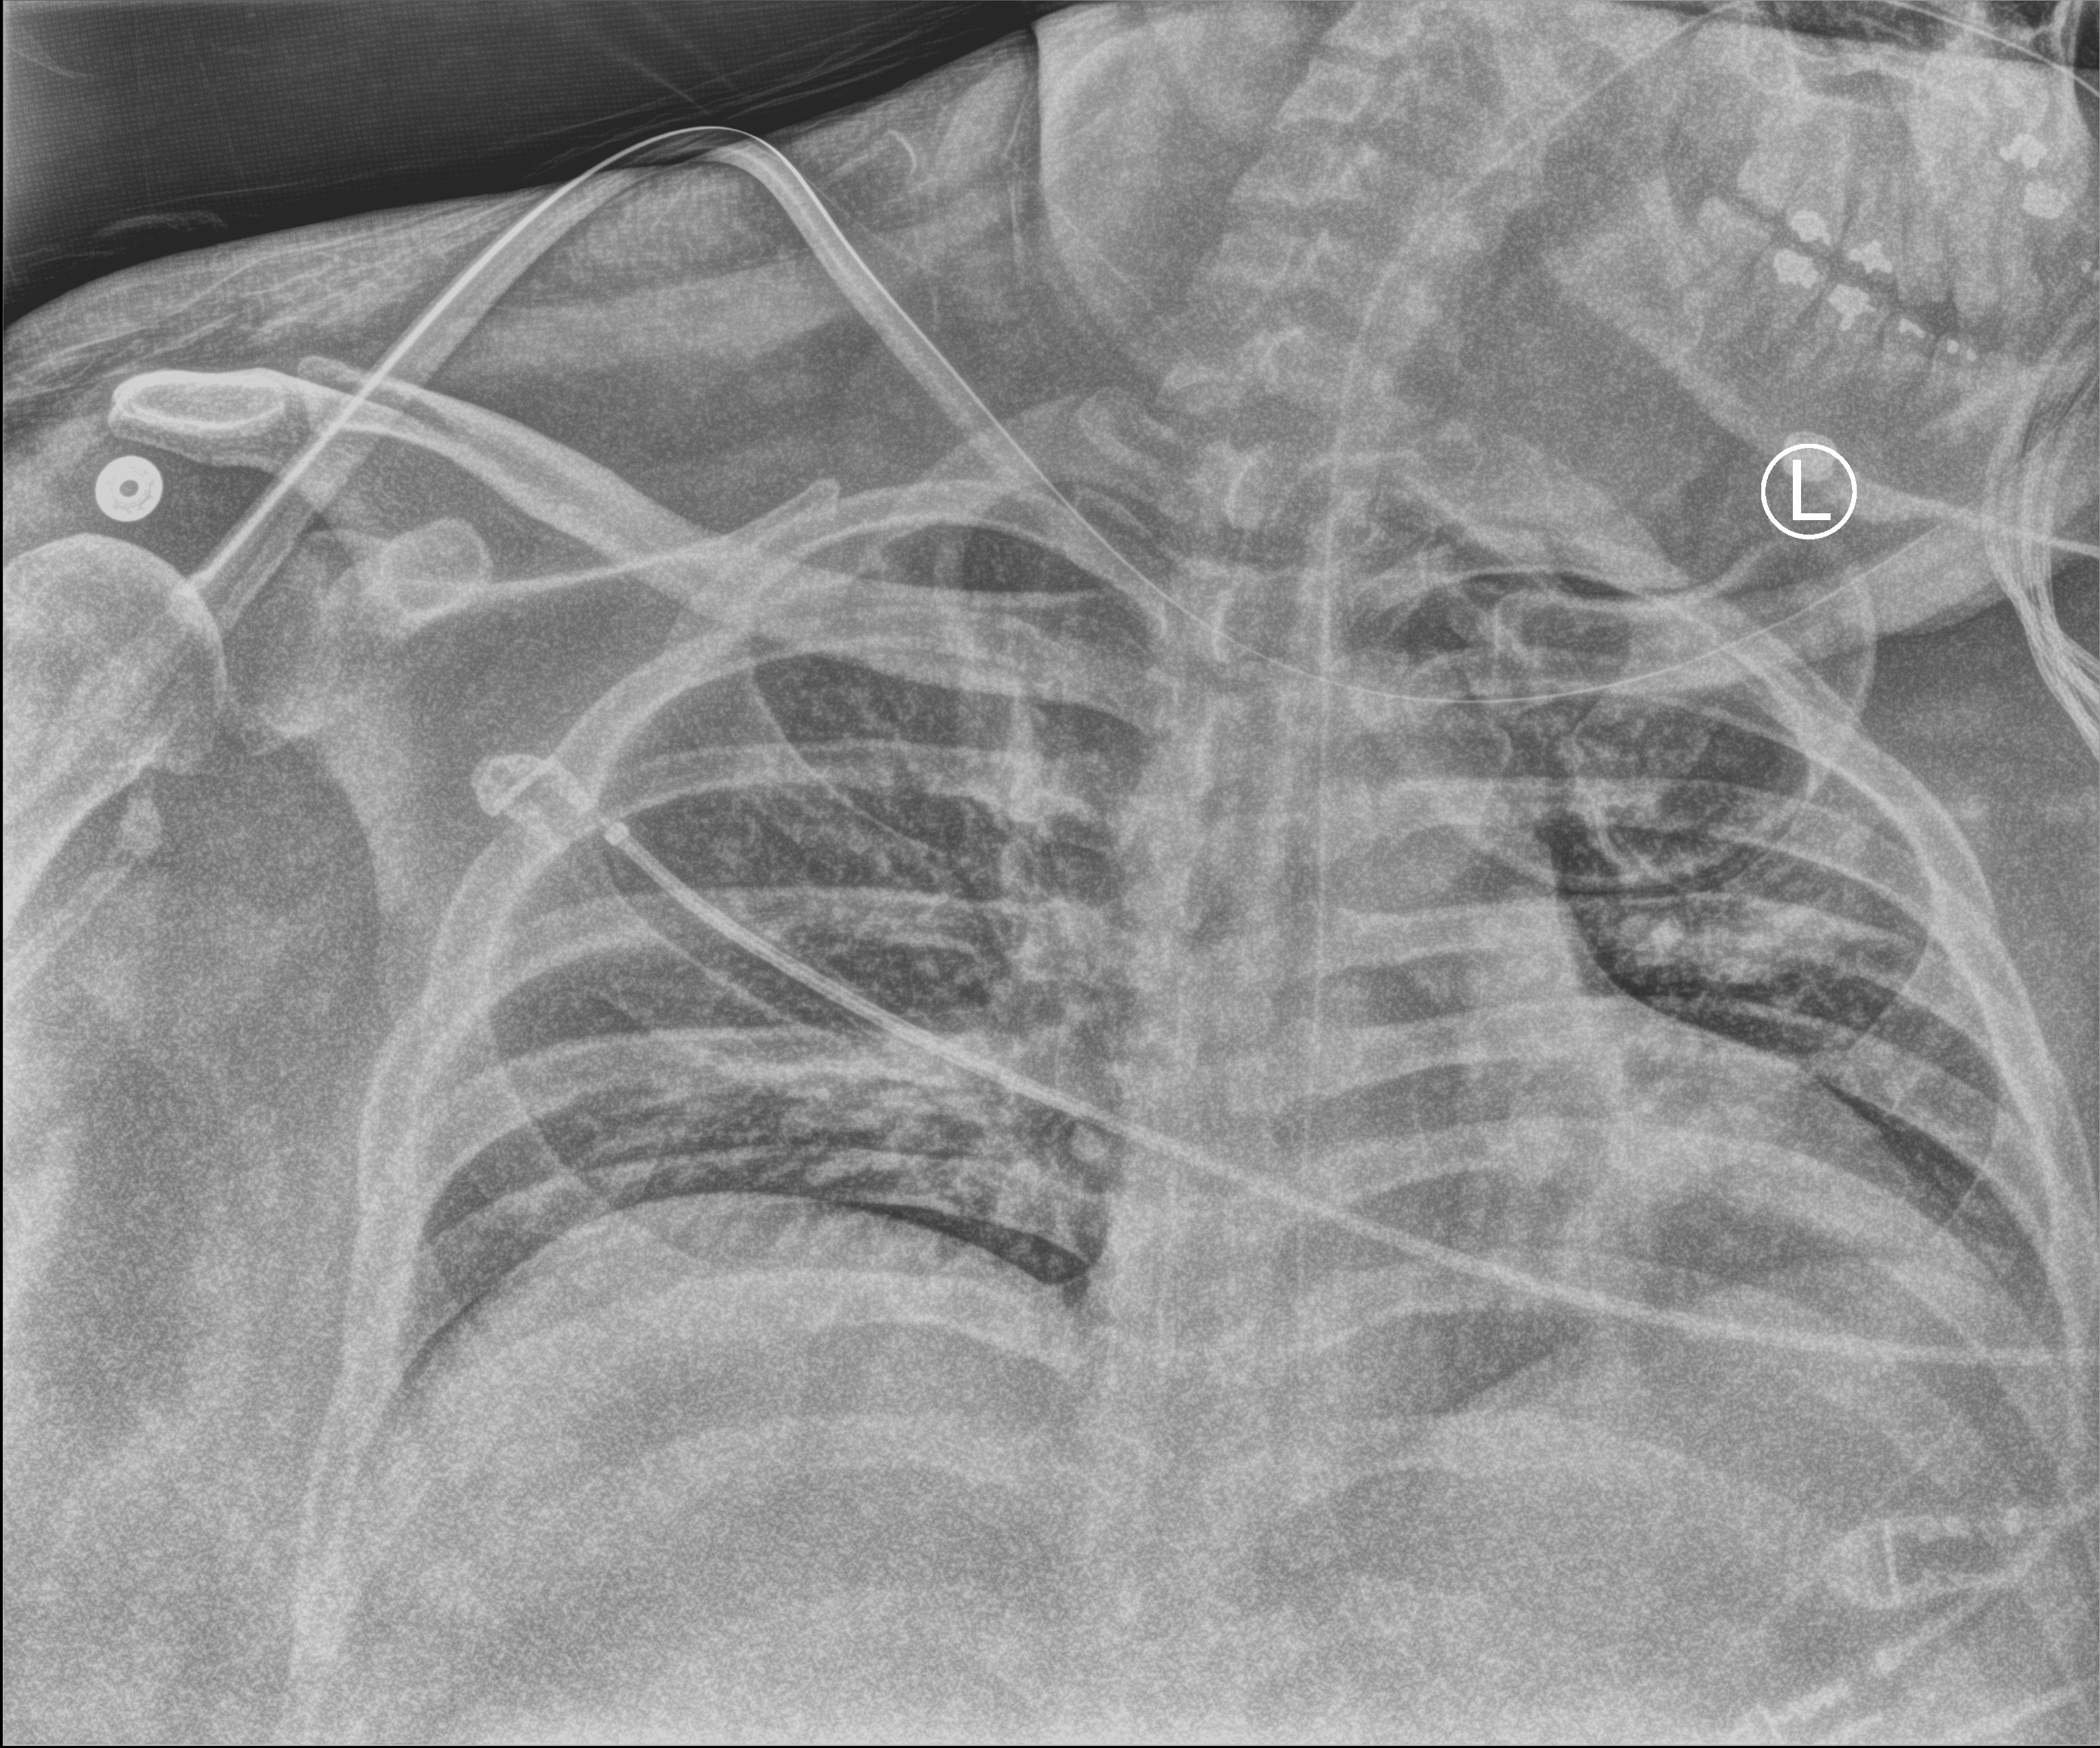
Bedside chest radiograph (computed radiography). Patient hospitalised with COVID-19; male, aged 18–59 years.
Hospital-stay facts (about this admission, not read from this image; timing relative to this image not recorded): hypertension (admission record): no.